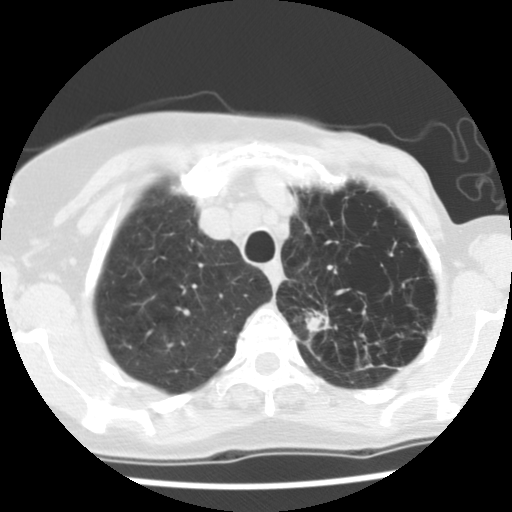
Low-dose screening chest CT, one axial slice; lung window (W 1500 / L -600 HU); 512 × 512 image matrix, field of view 290 × 290 mm.
Annotated regions visible in this slice (manually delineated by an expert):
- lesion 1 (tumor, upper lobe of left lung): box from (x=305, y=311) to (x=330, y=333) px